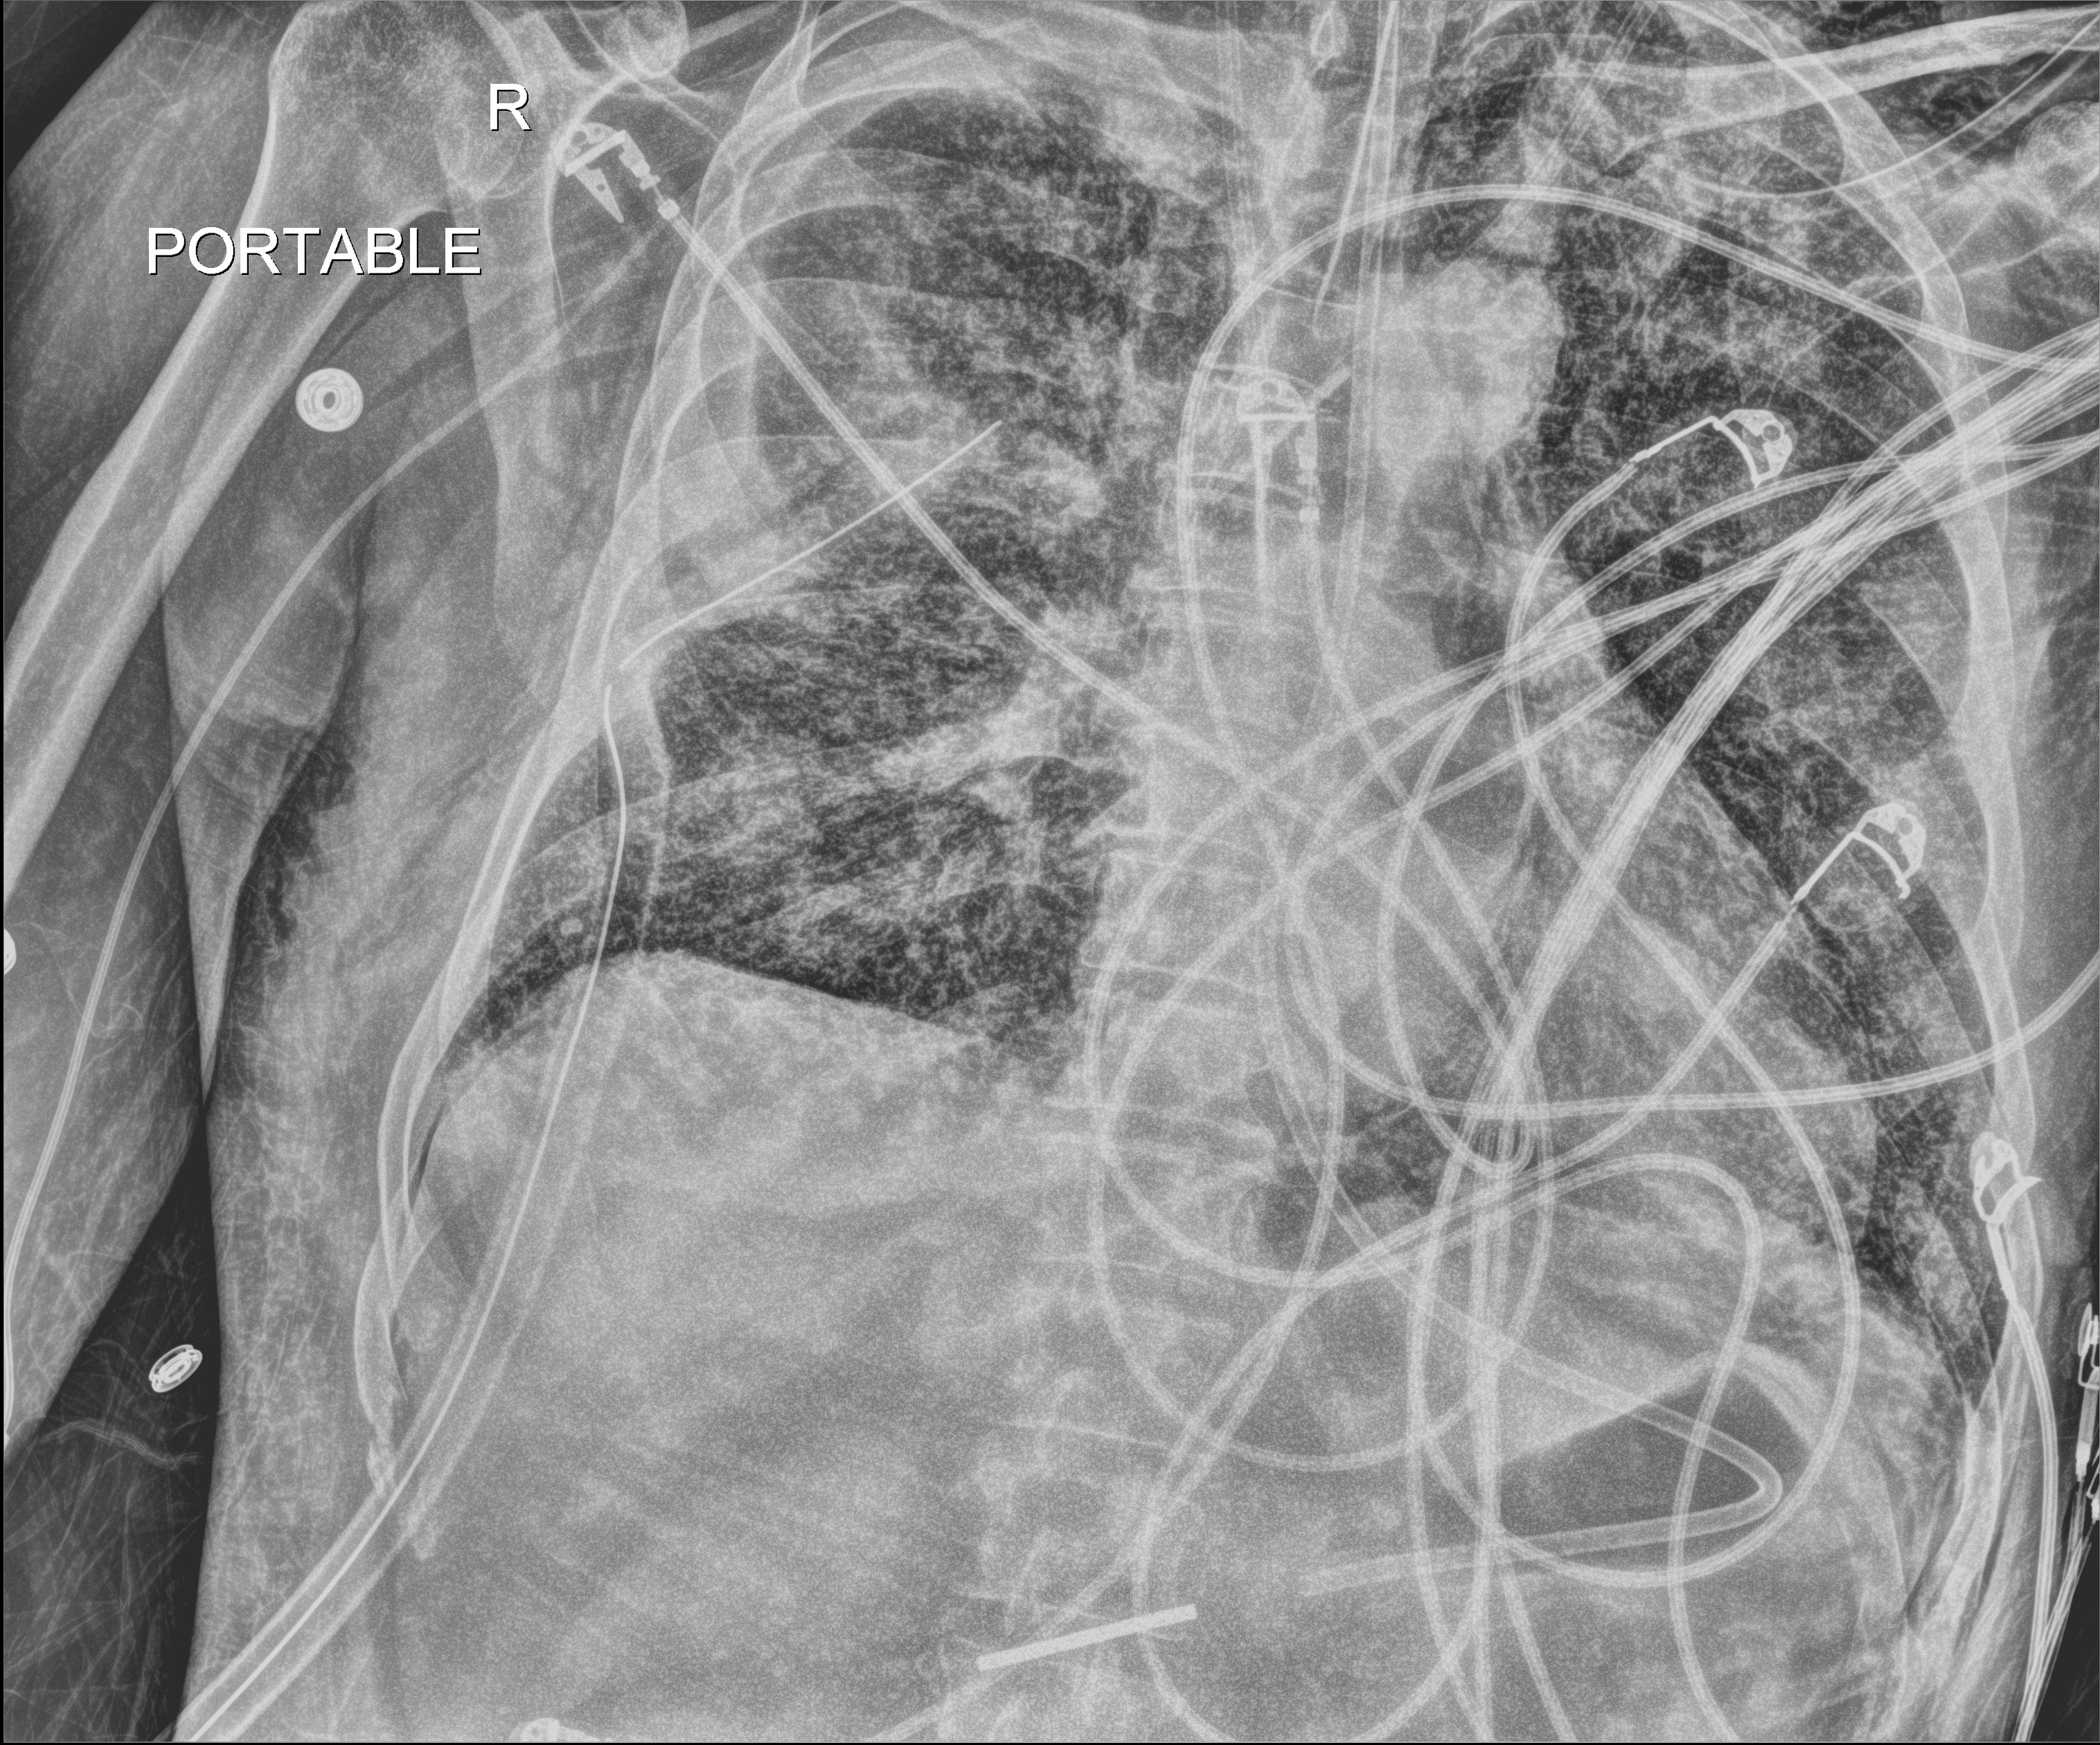
Portable chest radiograph, anteroposterior (AP) projection. Patient hospitalised with COVID-19; male, aged 18–59 years.
Hospital-stay facts (about this admission, not read from this image; timing relative to this image not recorded): length of hospital stay: 42 days; mechanically ventilated during this hospital stay: yes.